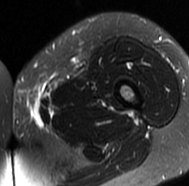
MRI of an extremity soft-tissue mass, one axial slice. Position 19 of 77 along the scan axis. T2-weighted fat-saturated. MR volume resampled by the dataset authors to the PET/CT grid (not the native acquisition matrix). 3.27 mm slice thickness. 189 × 186 image matrix, field of view 185 × 182 mm. Female patient. From the clinical record (not read from this slice): histological type: leiomyosarcoma; grade: high; site of the primary tumour: groin.
Outlined on this slice (expert contour drawn on MRI and transferred to this co-registered scan by the dataset authors):
- gross tumour volume including surrounding oedema: bounding box <12,86,52,126> (left, top, right, bottom; pixels)